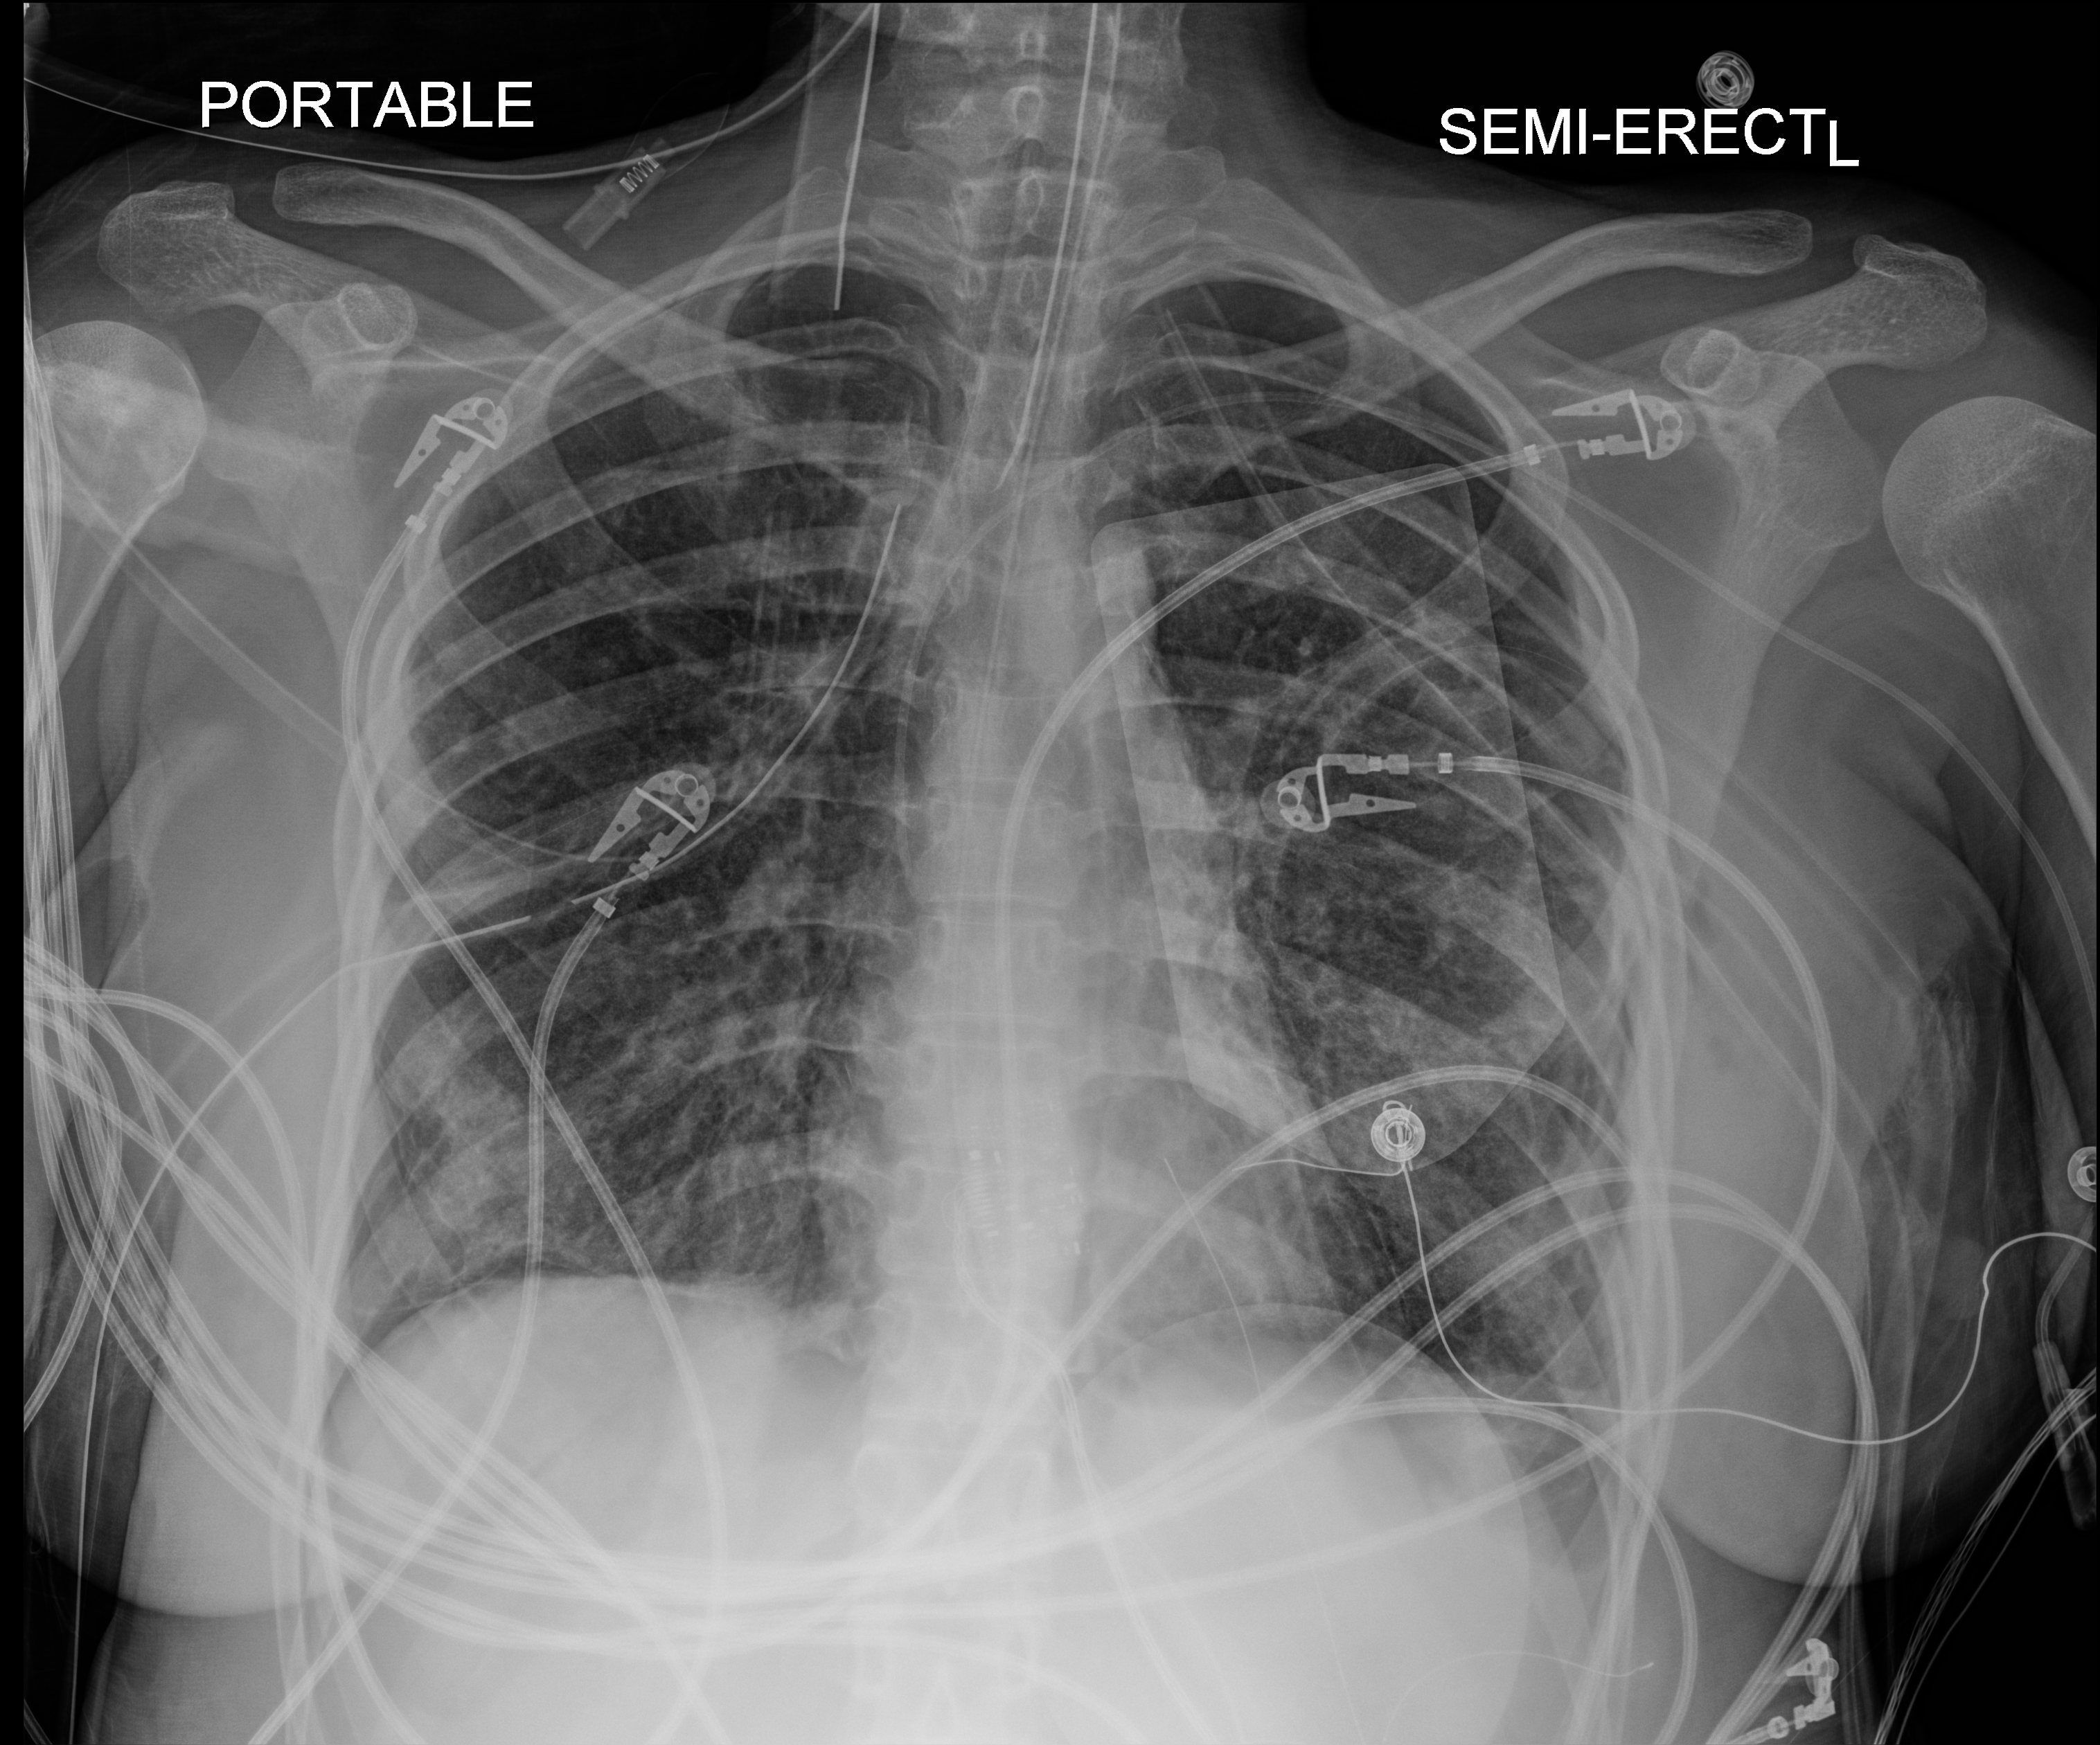
Bedside chest radiograph (digital radiography); anteroposterior (AP) projection. Patient hospitalised with COVID-19, aged 18–59 years.
Hospital-stay facts (about this admission, not read from this image; timing relative to this image not recorded):
- mechanically ventilated during this hospital stay: yes